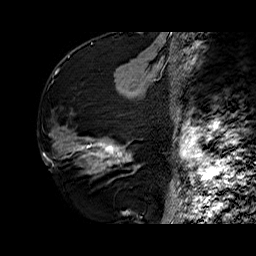
Breast MRI (dynamic contrast-enhanced), one sagittal slice. Slice 26 of 60 in the series (ordered by position). Dynamic contrast-enhanced series, time point 2 of 6 at this slice position (early post-contrast). 1.5 T. TE 6.4 ms, TR 32.7 ms. 4 mm slice thickness. 256 × 256 image matrix. Female patient. From the clinical record (not read from this slice): setting: breast cancer imaged before/during neoadjuvant chemotherapy; receptor status: HR-positive, HER2-negative.
Annotated regions visible in this slice (semi-automatic segmentation, software-assisted and operator-edited):
- analysis volume of interest (the breast-tissue region the enhancement analysis was run in; not a lesion): bounding box (x1, y1, x2, y2) in pixels: (73, 133, 141, 176)
- tumour enhancement mask (voxels above the 100 % enhancement threshold inside the analysis volume of interest): (87, 138, 131, 166)